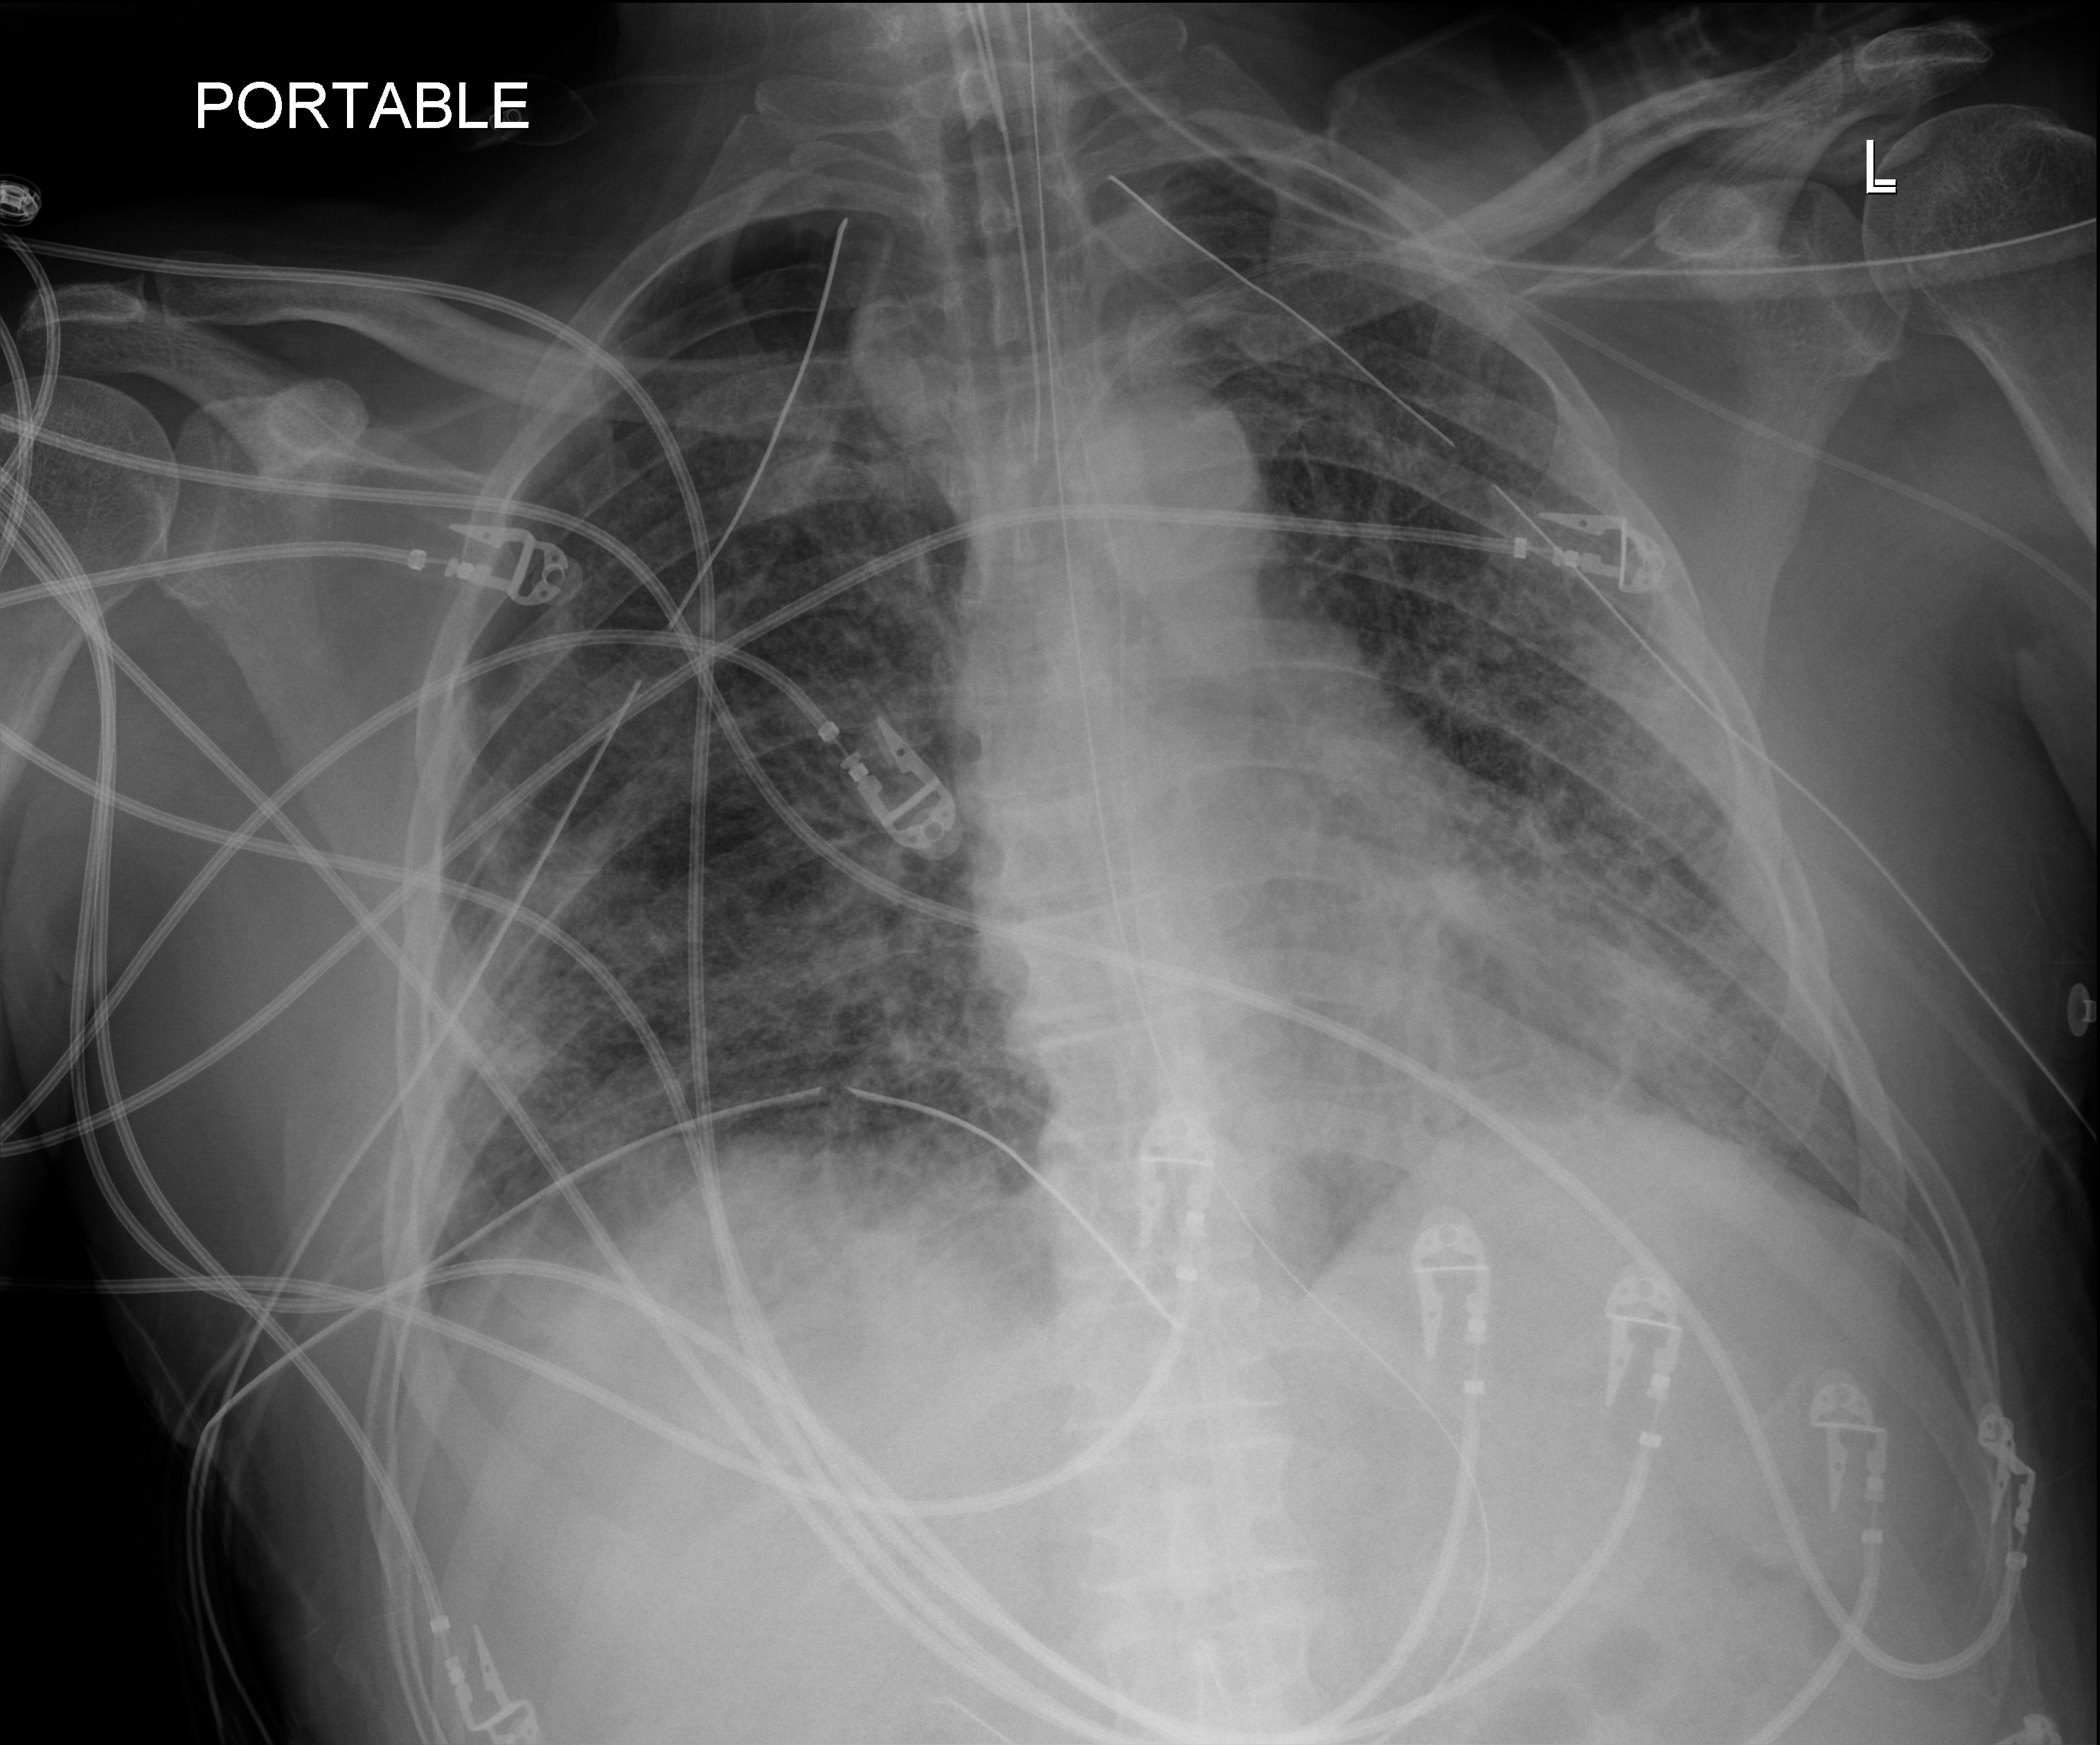
Portable chest radiograph, anteroposterior (AP) projection. Male patient hospitalised with COVID-19, age 18–59 years.
From the hospital-stay record, not from the radiograph (when in the stay this image was taken is not recorded): admitted to intensive care during this hospital stay: yes; mechanically ventilated during this hospital stay: yes.